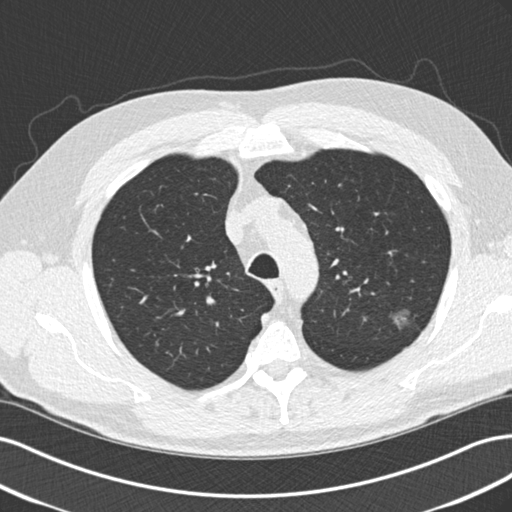
Low-dose screening chest CT, one axial slice; position 163 of 209 along the scan axis; reconstruction kernel B30f; lung window (W 1500 / L -600 HU); 2 mm slice thickness; 512 × 512 image matrix, field of view 360 × 360 mm.
Structures marked on this image (expert manual segmentation):
- lesion 1 (tumor, upper lobe of left lung): bounding box <391,309,409,329> (left, top, right, bottom; pixels)